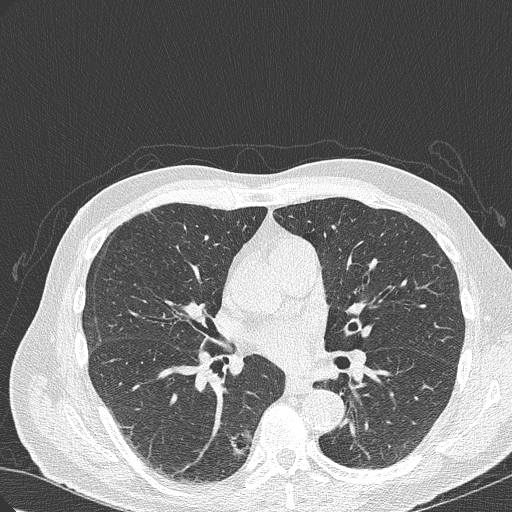
Chest CT (low-dose screening protocol), one axial image; baseline annual screen; lung window (W 1500 / L -600 HU); 512 × 512 image matrix, field of view 350 × 350 mm. Male participant, aged 70 years at enrolment. Current smoker at enrolment.
- Lesion marked by an expert reader, box from (x=197, y=420) to (x=260, y=481) px.
- The screening reader recorded 4 non-calcified nodules or masses ≥4 mm on this exam (right lower lobe, right lower lobe, right upper lobe, right lower lobe); which of them this box marks is not recorded.
- Official screen result: positive, change unspecified: nodule(s) >= 4 mm or enlarging nodule(s), mass(es), or other non-specific abnormalities suspicious for lung cancer.
- Later outcome: lung cancer diagnosed 978 days after this screen — bronchiolo-alveolar adenocarcinoma, NOS, right lower lobe, poorly differentiated (G3), stage IB (AJCC 6th edition), 30 mm at pathology.